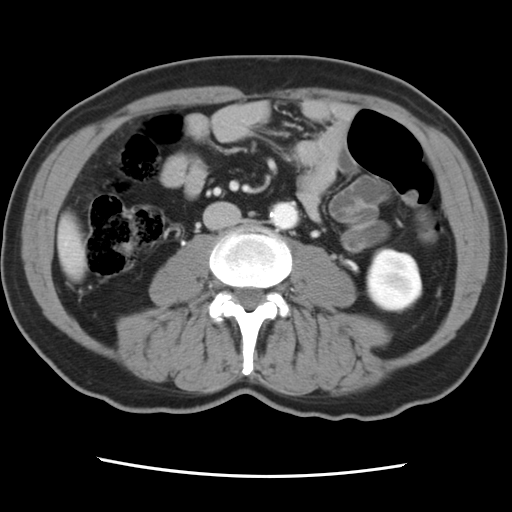
Contrast-enhanced abdominal CT, one axial slice. Position 14 of 83 along the scan axis. 120 kVp. Intravenous contrast given. Soft-tissue window (W 400 / L 40 HU). 512 × 512 image matrix, field of view 321 × 321 mm. Male patient, age 69 years. From the clinical record (not read from this slice): diagnosis: colorectal cancer liver metastases, imaged before liver resection; multiple liver metastases: yes; largest metastasis: 3.5 cm; chemotherapy before resection: yes.
Outlined on this slice (expert manual segmentation):
- liver: bounding box (x1, y1, x2, y2) in pixels: (60, 219, 85, 276)
- planned liver remnant (the part of the liver to remain after resection): (60, 219, 86, 276)